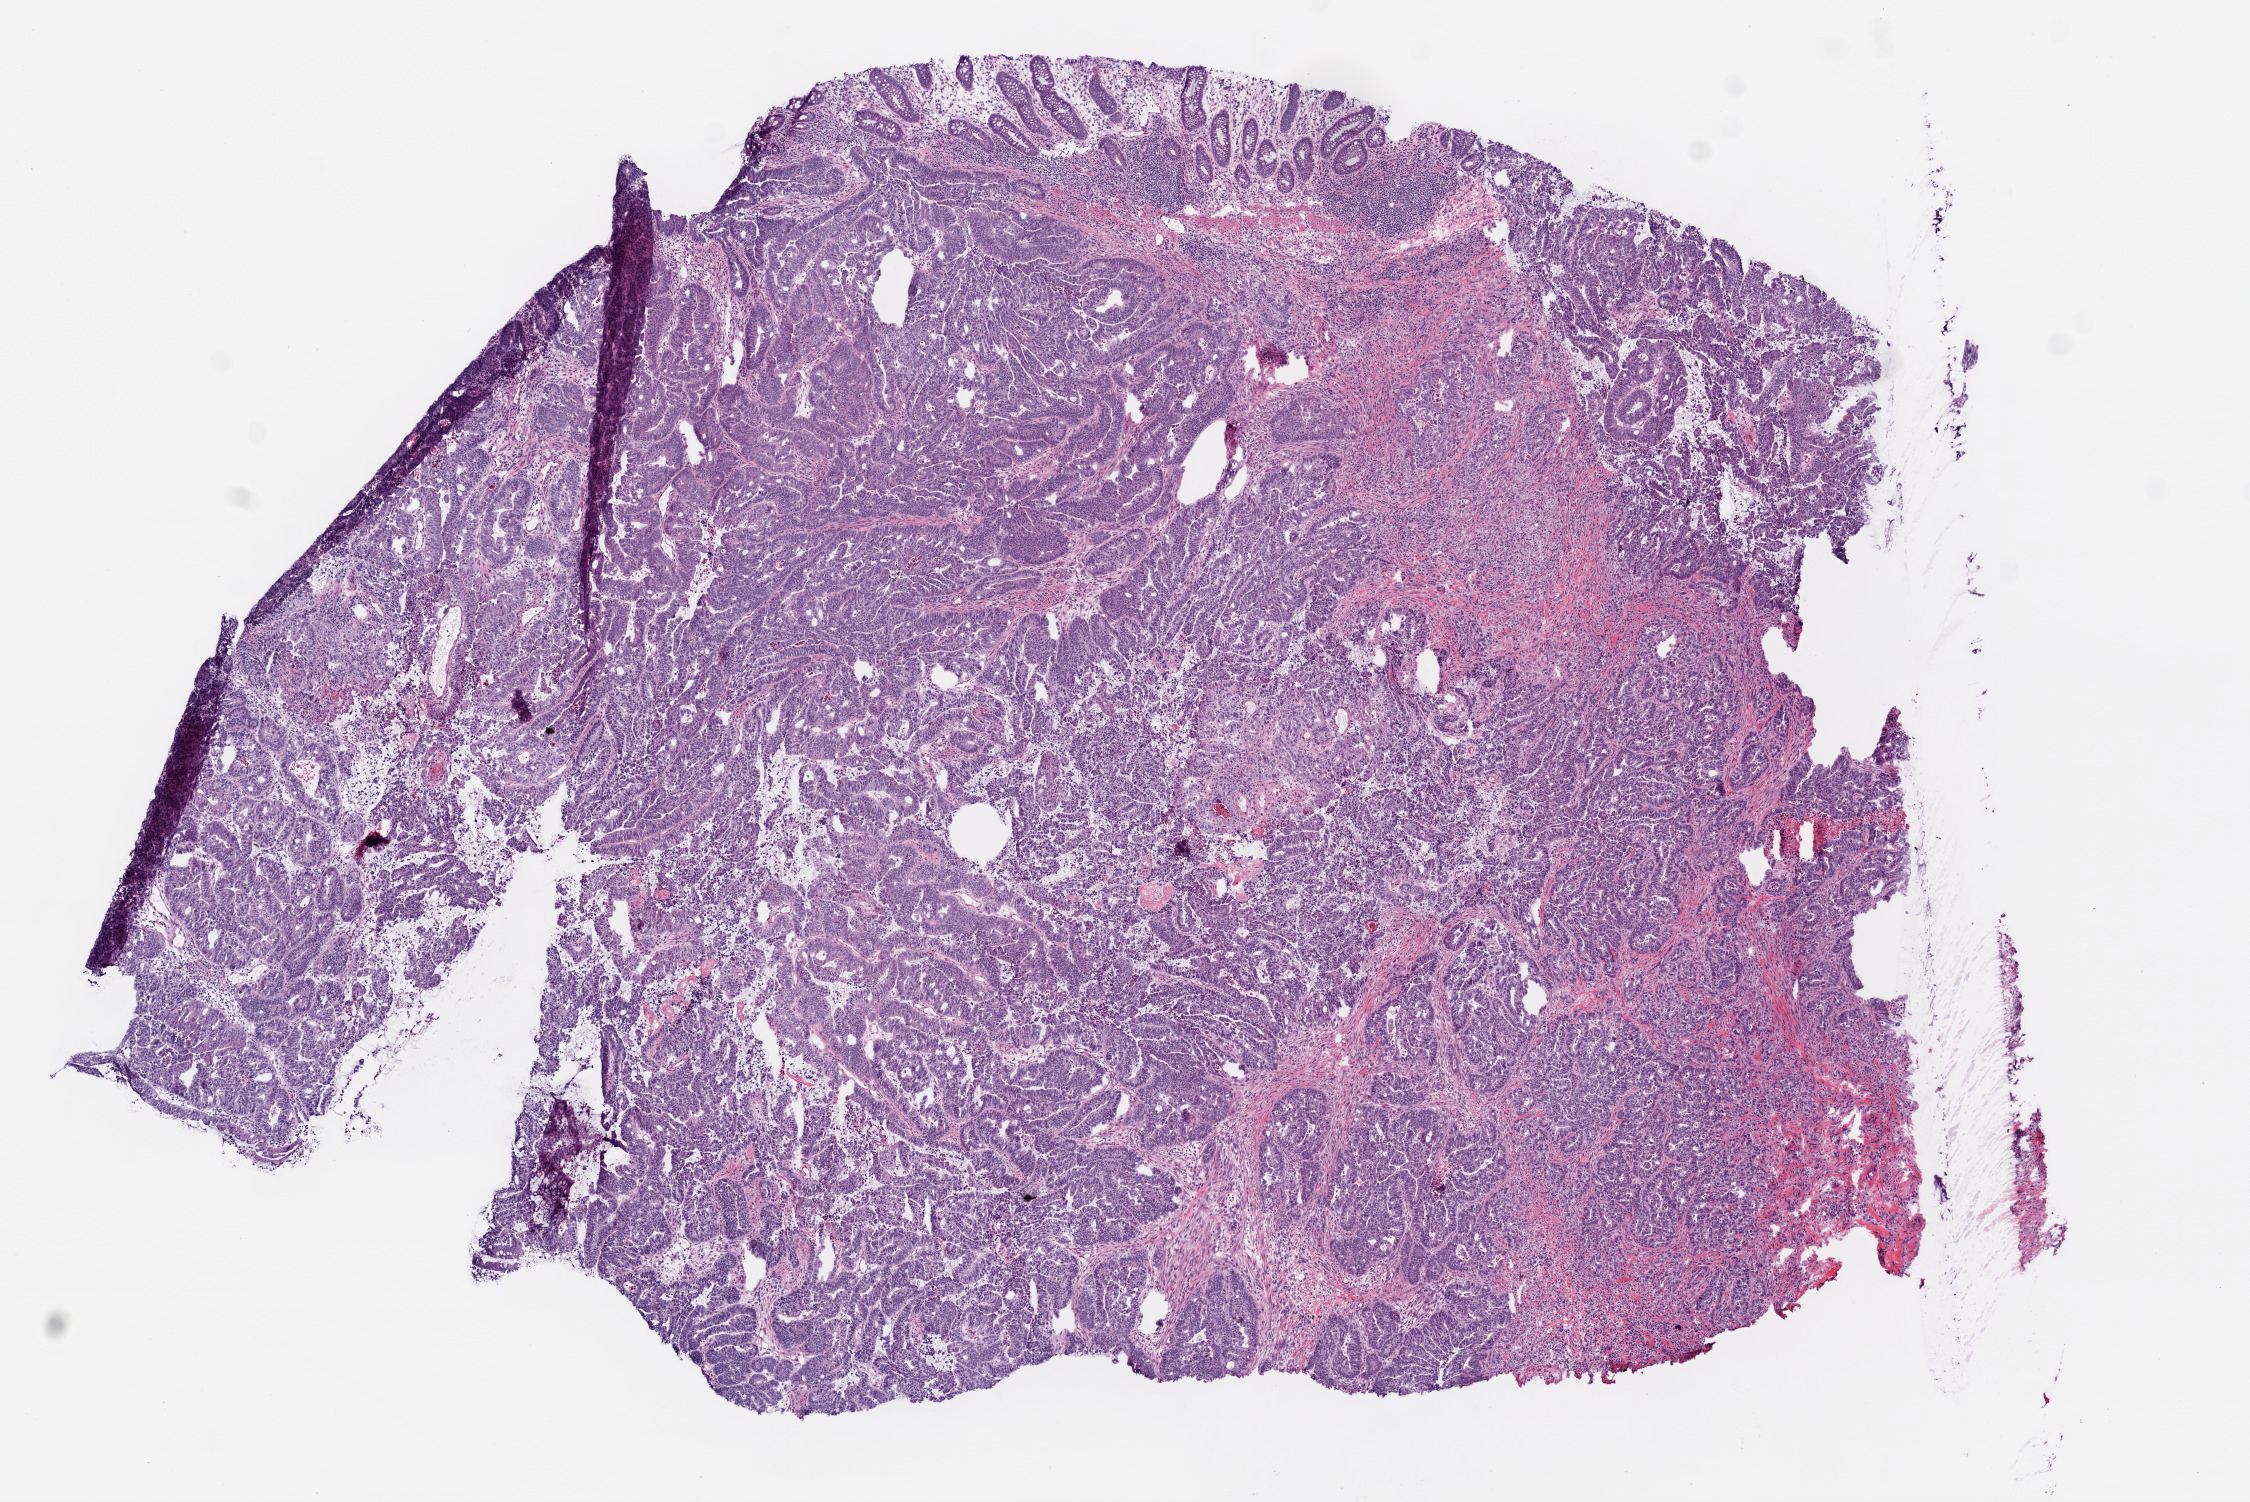
Whole-slide histology image, H&E — low-resolution overview of the scanned area, about 9.0 x 6.0 mm (slide scanned at 20x); frozen section; rectum, primary tumour sample. Female patient; age at initial diagnosis 85 years. Composition of this section per pathologist review: tumour cells 75%, tumour nuclei 80%, normal cells 8%, stromal cells 15%, necrosis 2%.
- AJCC pathologic stage: IIA (6th edition)
- pathologic diagnosis: Adenocarcinoma, NOS (colon, NOS)
- lymph nodes positive (case pathology): 0 of 24 examined